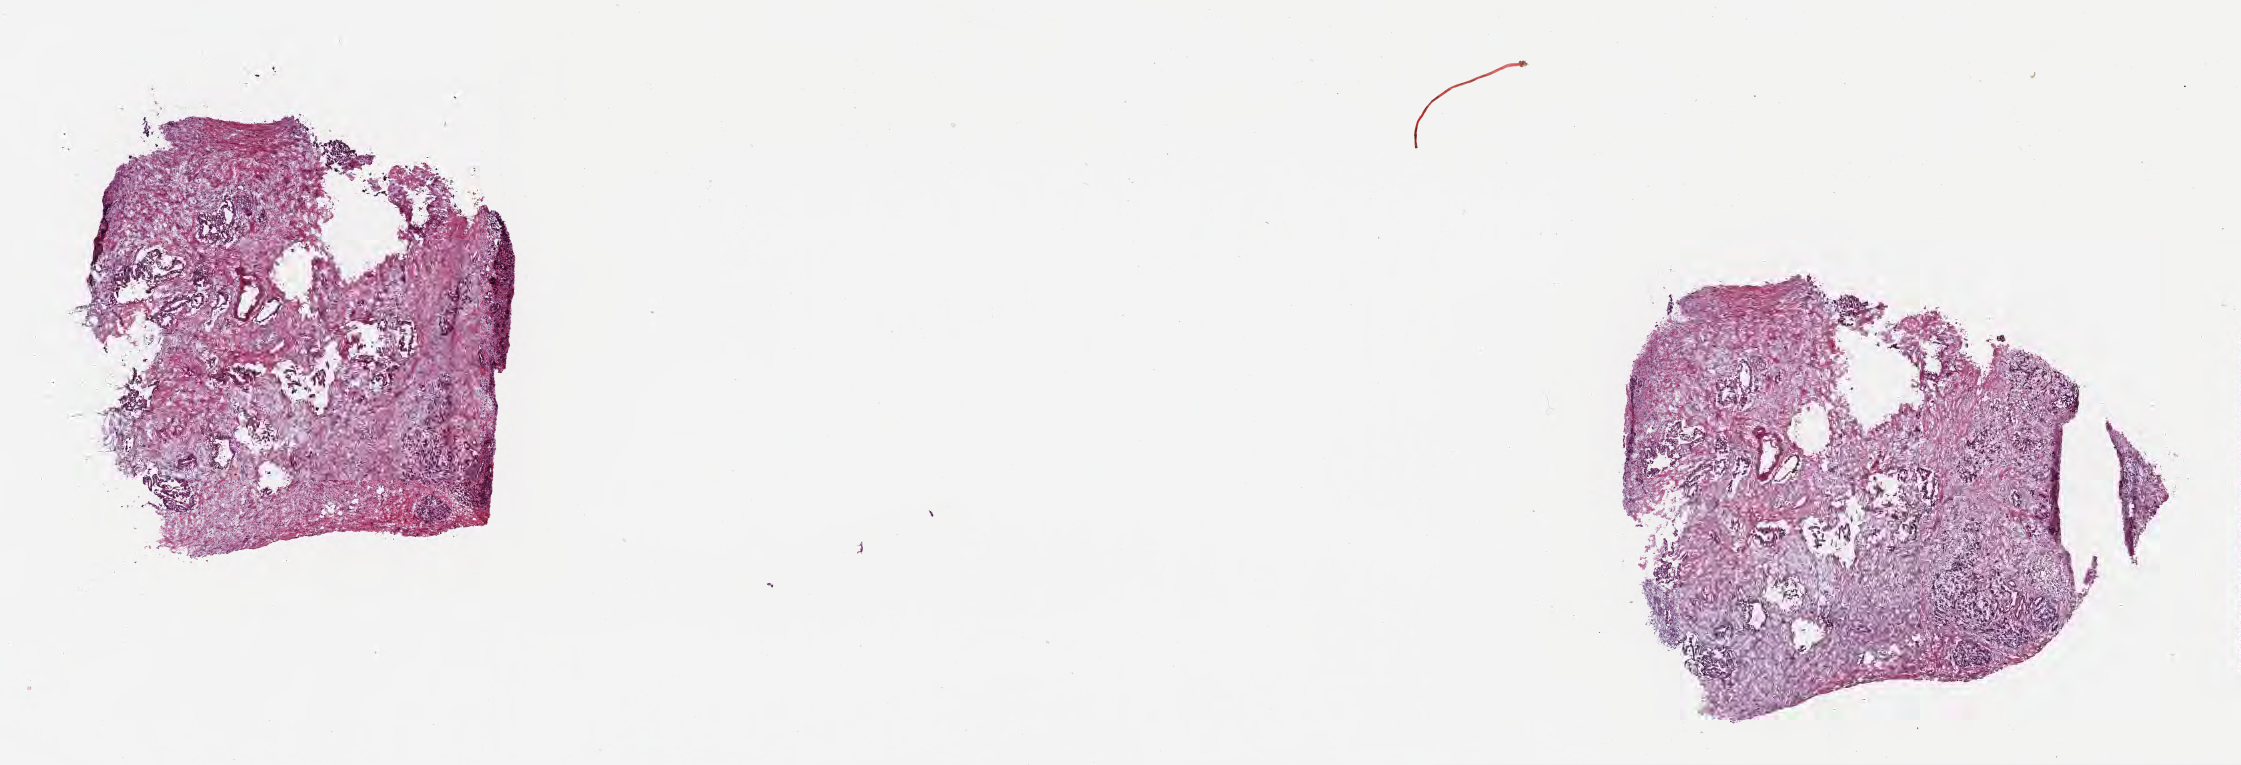
Digitized H&E-stained section, low-resolution overview of the scanned area, about 18.1 x 6.2 mm. Cryosection. Specimen: primary tumor. Site: head of pancreas. Male, age 75 years at initial diagnosis. Tumor grade: G2 (moderately differentiated). Slide review estimates, as recorded: tumor cells 18%, tumor nuclei 40%, stromal cells 67%, necrosis 0%, normal cells 15%. Inflammatory infiltration, as recorded: lymphocyte infiltration 26%, monocyte infiltration 3%, neutrophil infiltration 0%.
Diagnosis: Infiltrating duct carcinoma, NOS. AJCC pathologic stage: Stage III.